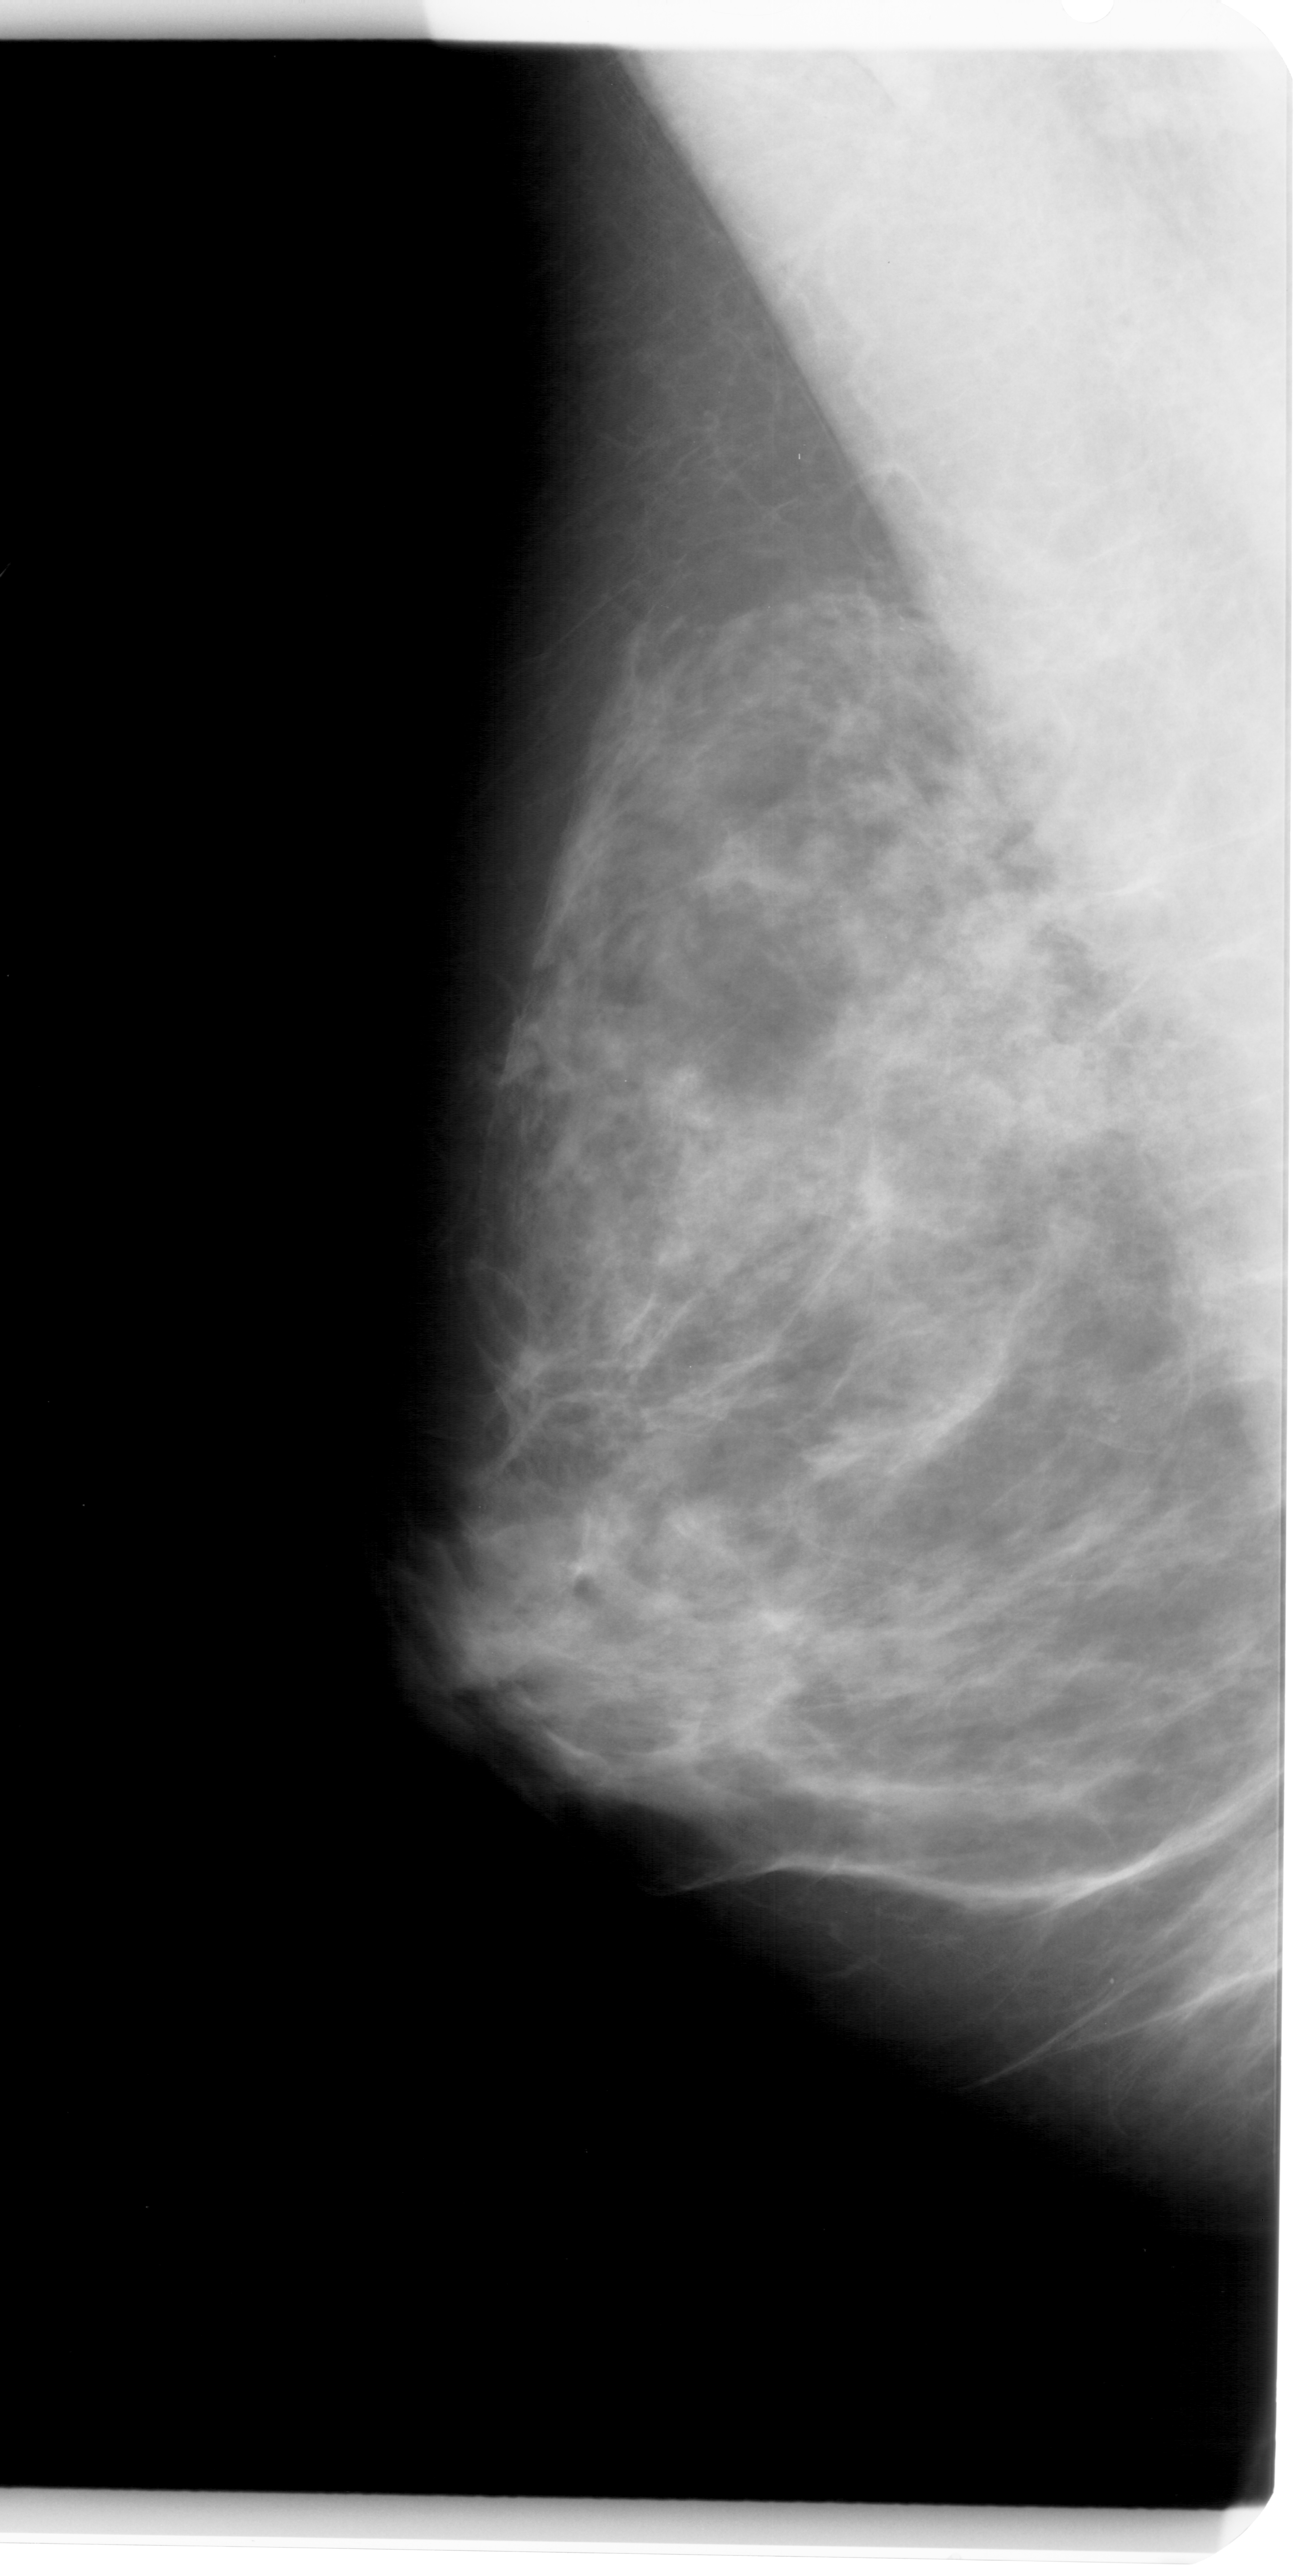
Digitized screen-film mammogram; left breast; mediolateral oblique (MLO) view; BI-RADS breast density category 4 (scale 1–4); 1309 × 2576 image matrix.
Marked abnormalities (boxes around the expert regions of interest):
- calcifications, morphology pleomorphic, distribution clustered; BI-RADS assessment category 3; subtlety rating 2 on a 1 (subtle) to 5 (obvious) scale; pathology result (as recorded, not read from the image): benign: box from (x=813, y=560) to (x=996, y=712) px